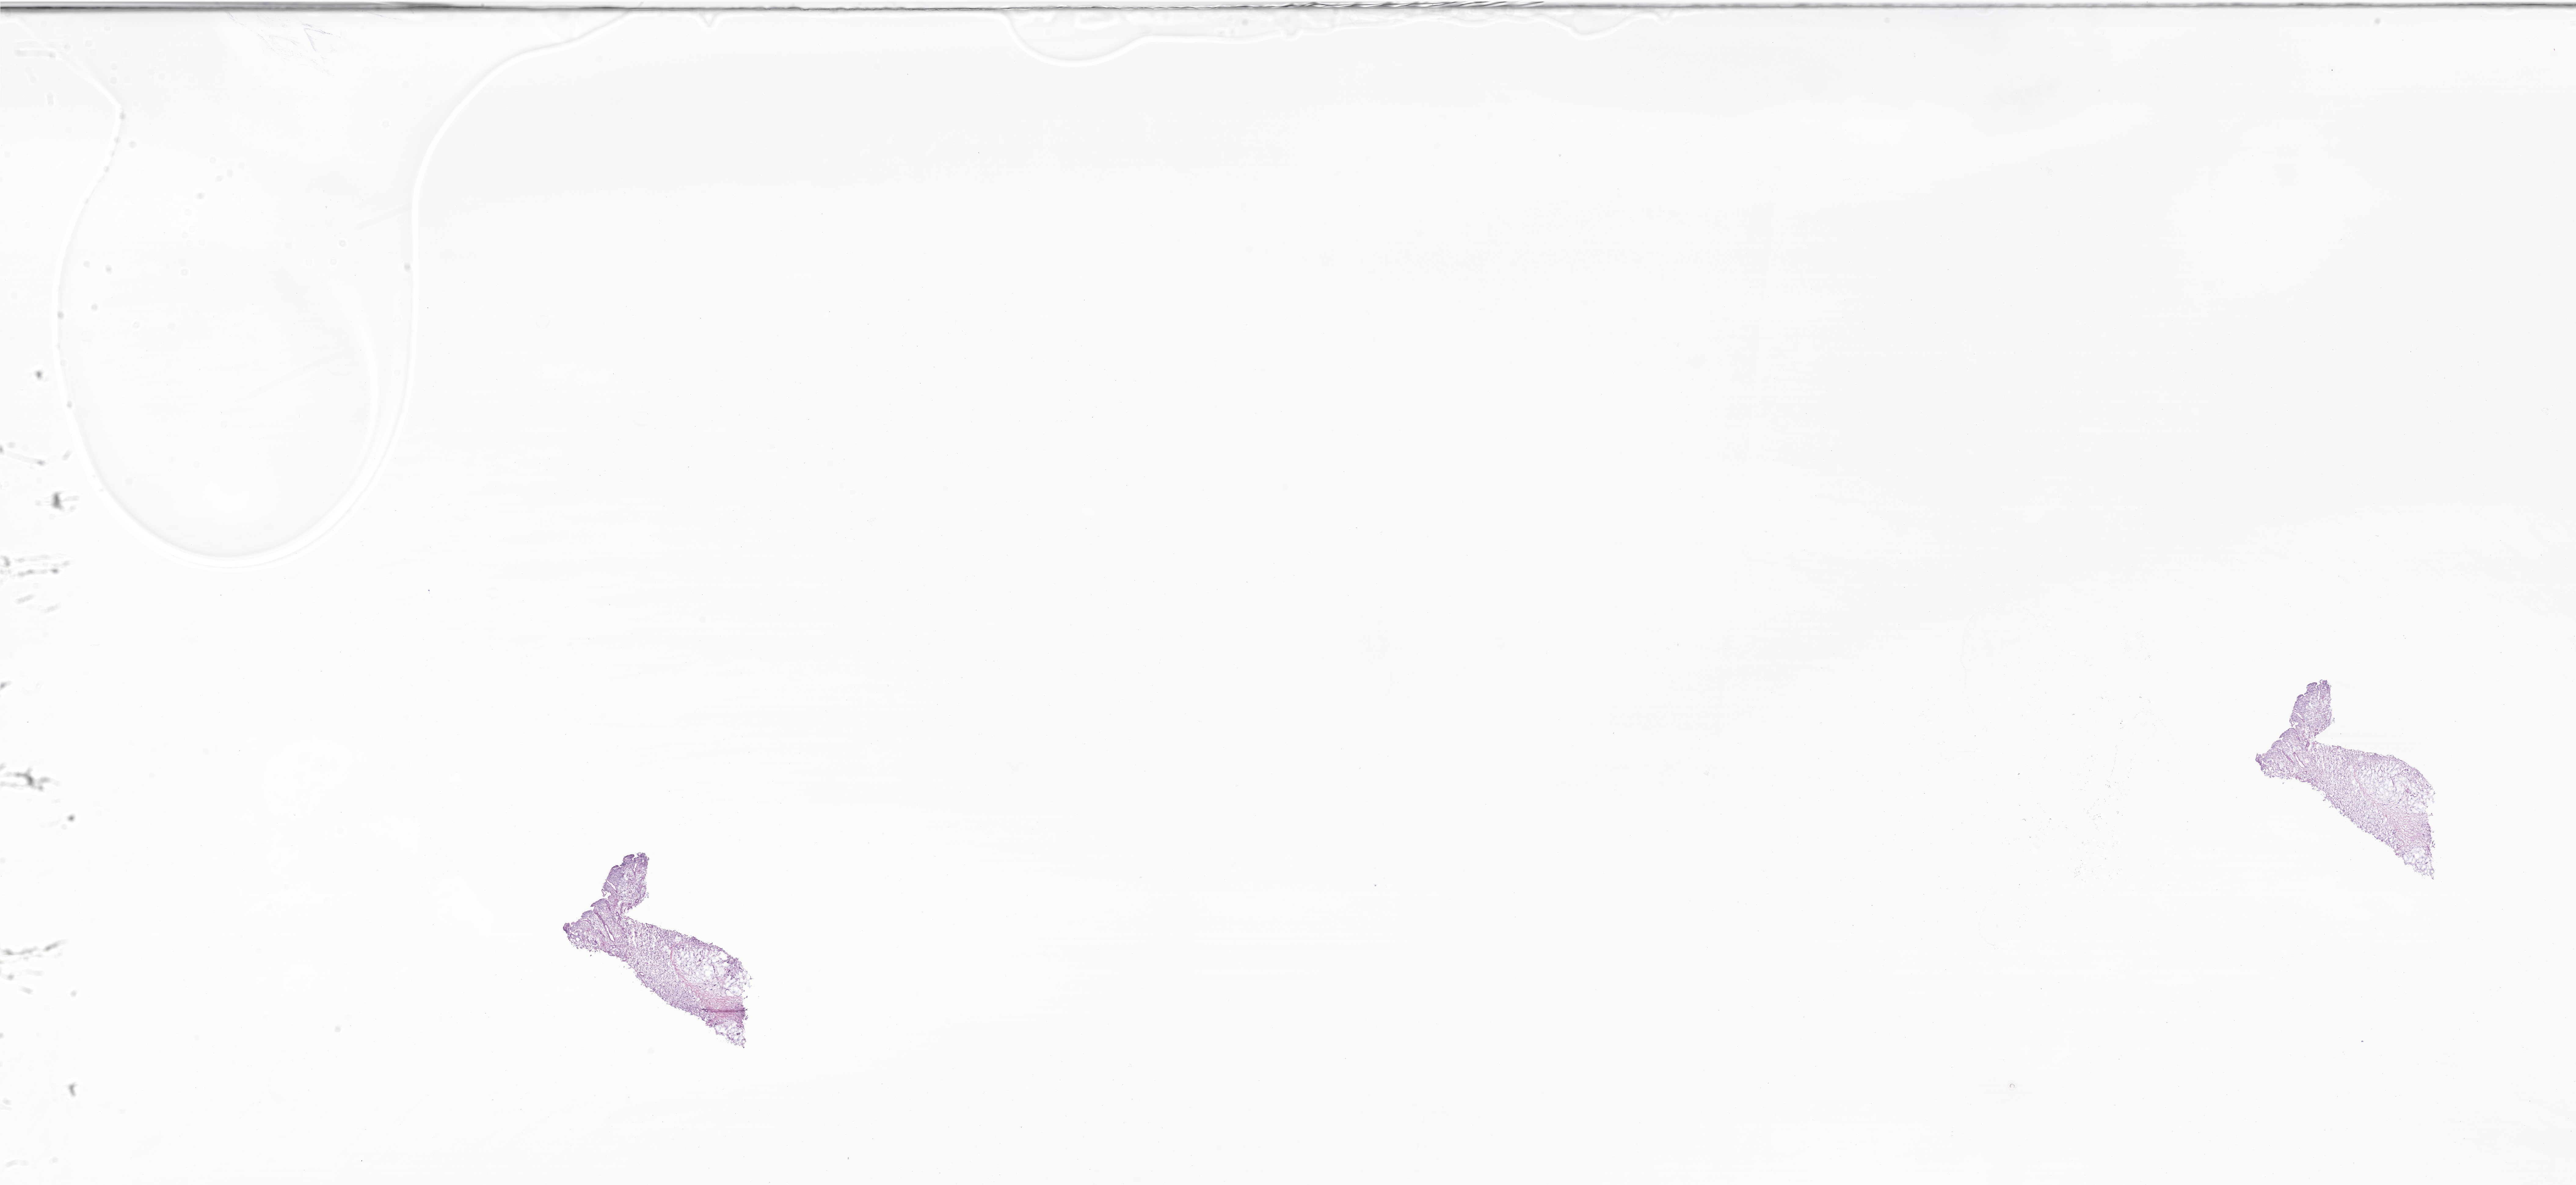
Whole-slide image, hematoxylin and eosin (H&E) stain of tumor tissue from the small intestine, low-resolution overview of the scanned area, about 35.6 x 16.4 mm; cryosection (OCT / tissue freezing medium). Female patient, age 201 months (16 years 9 months).
• diagnosis (ICD-O-3 morphology term): Signet ring cell carcinoma